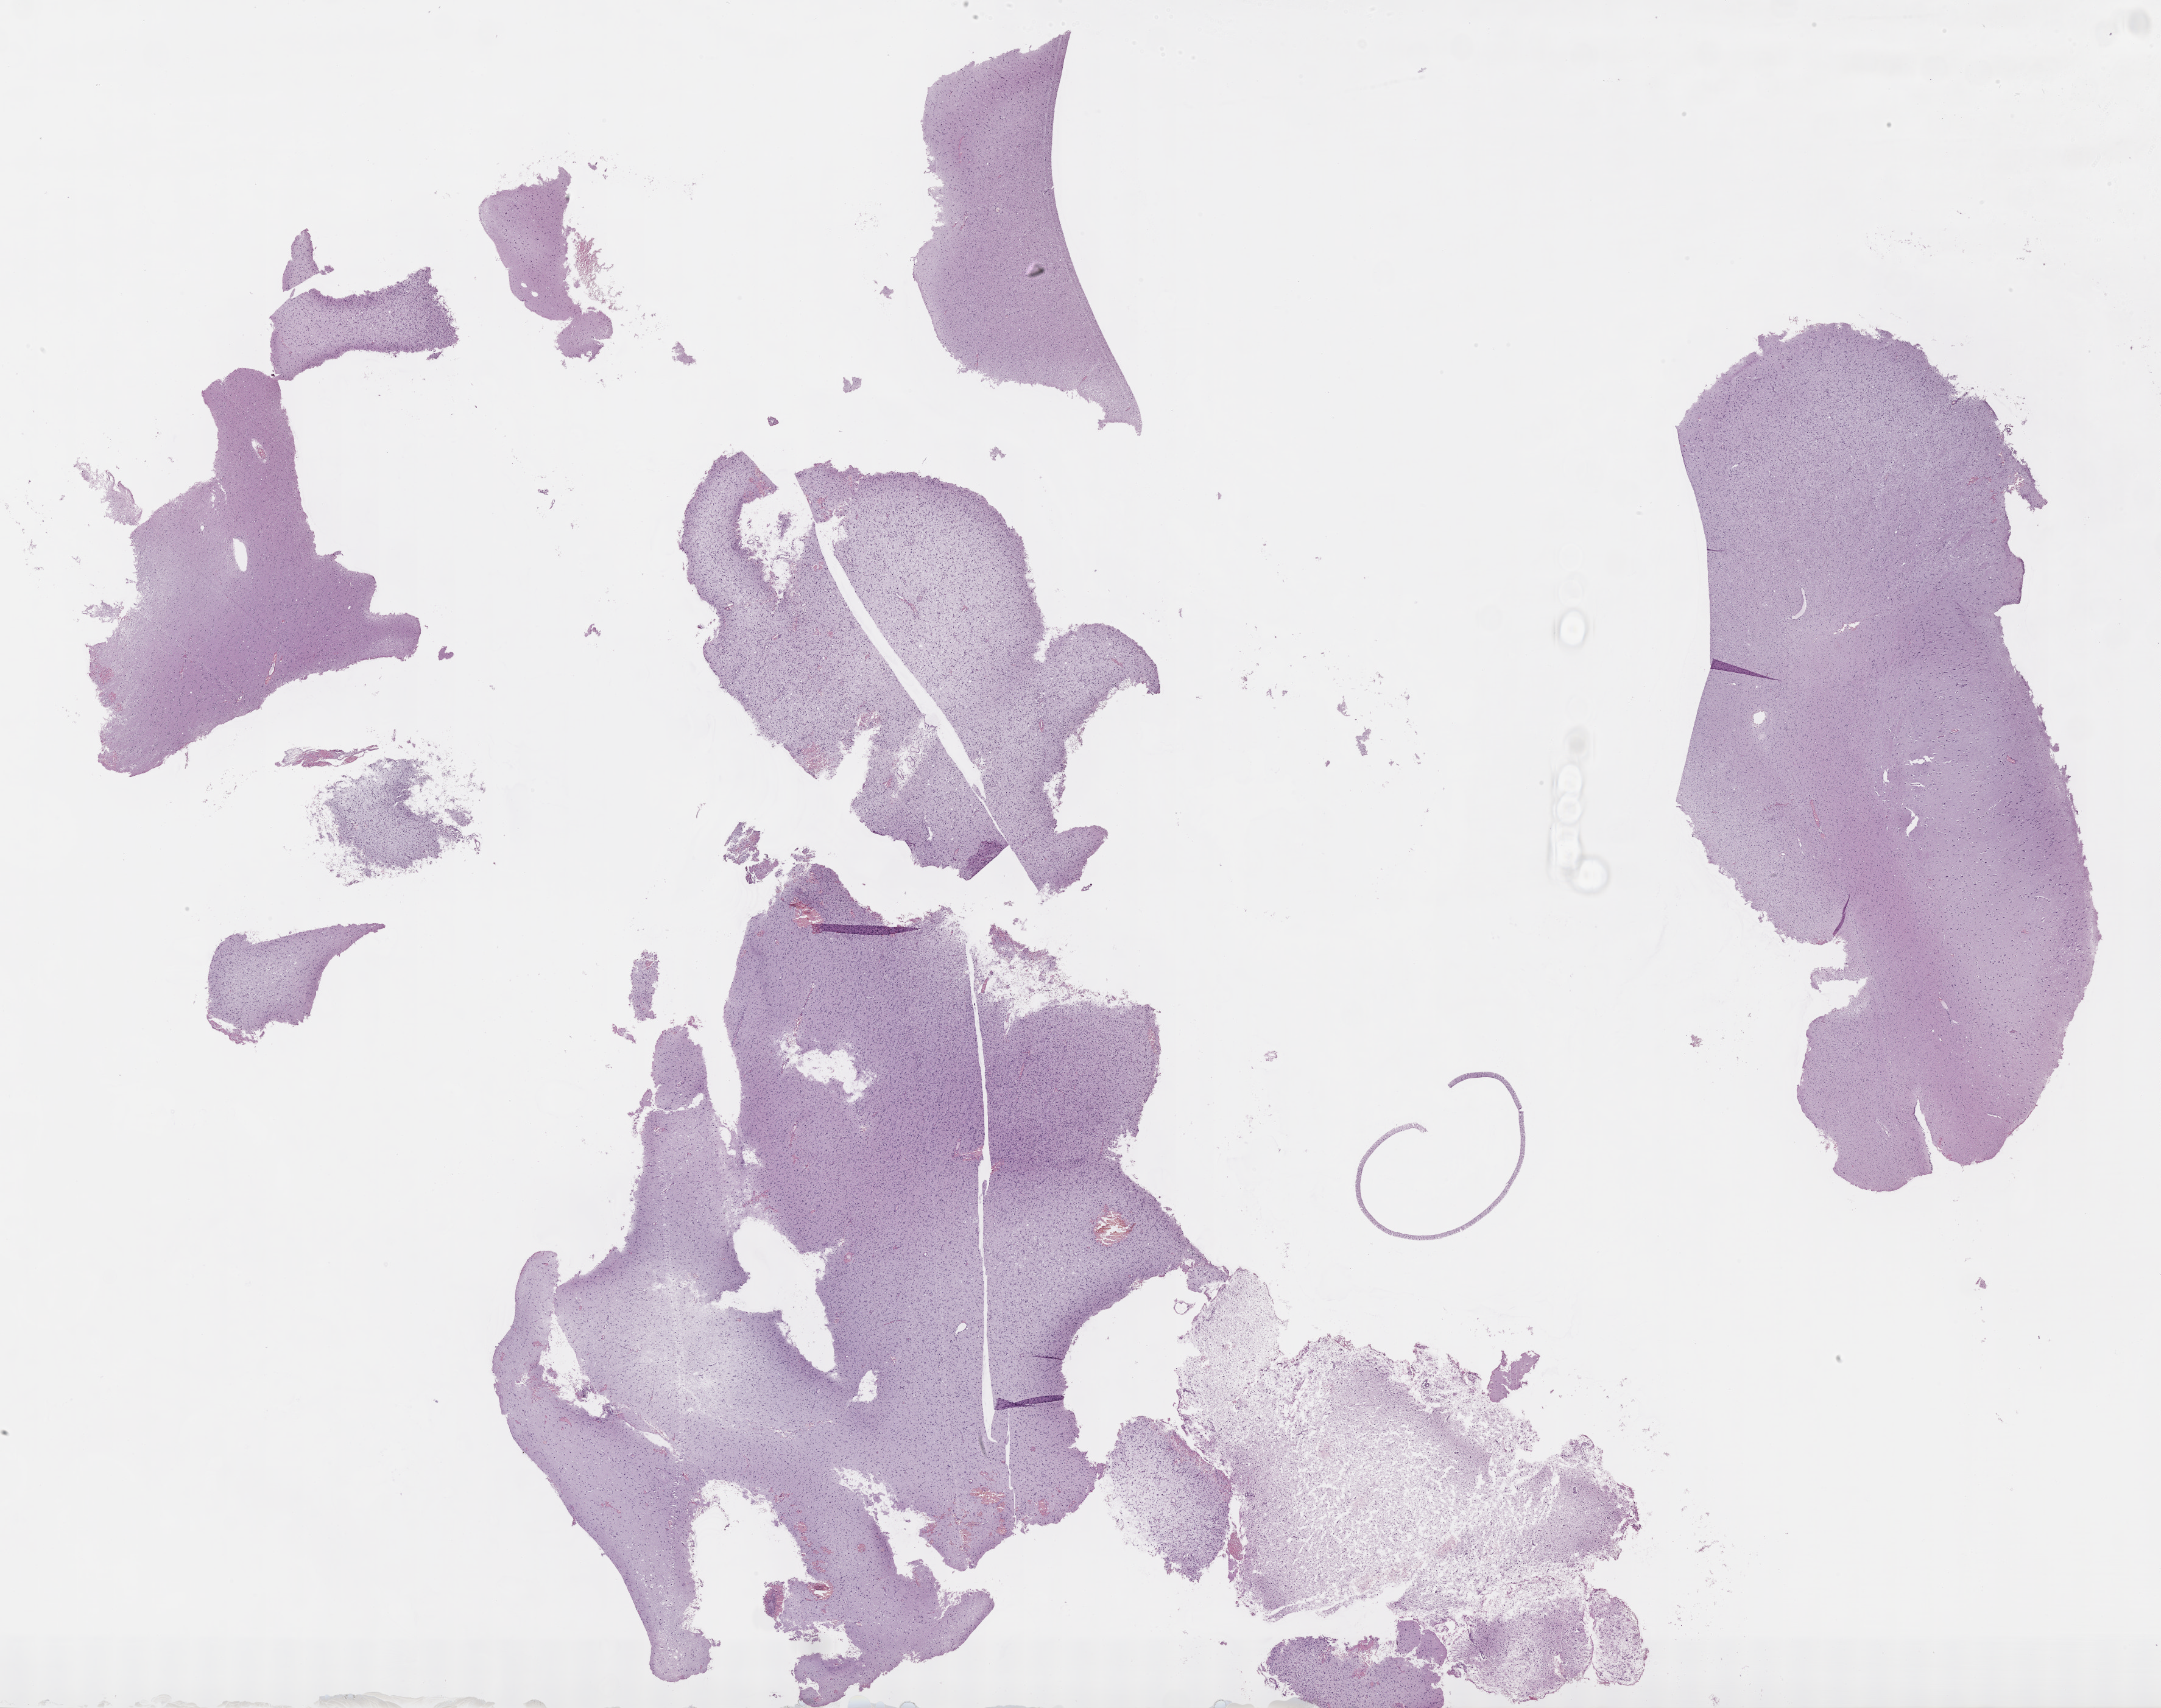
Whole-slide histology image, H&E-stained, whole scanned area (about 28.7 x 22.7 mm) shown as a low-resolution overview. FFPE section. Primary tumour sample from the brain. Female, age 44 years at initial diagnosis. Histologic grade: G3 (poorly differentiated).
• diagnosis: Astrocytoma, anaplastic